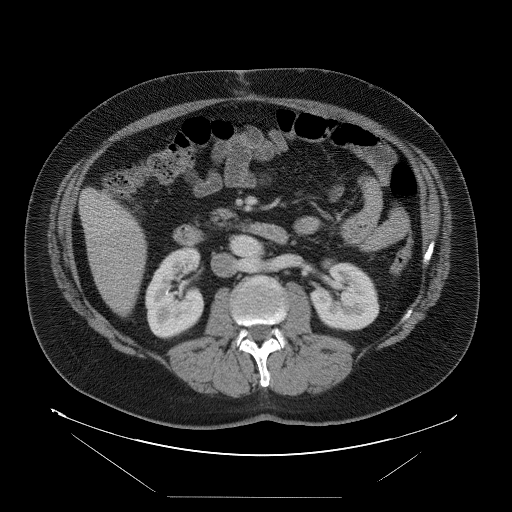
Contrast-enhanced abdominal CT, one axial slice. Slice 28 of 114 in the series (ordered by position). 120 kVp. Intravenous contrast given. Soft-tissue window (W 400 / L 40 HU). 5 mm slice thickness. 512 × 512 image matrix, field of view 500 × 500 mm. Male patient, age 61 years. Case-level facts recorded for this patient, not image findings: diagnosis: colorectal cancer liver metastases, imaged before liver resection; multiple liver metastases: no.
Structures marked on this image (expert manual segmentation):
- liver: bounding box <81,189,147,315> (left, top, right, bottom; pixels)